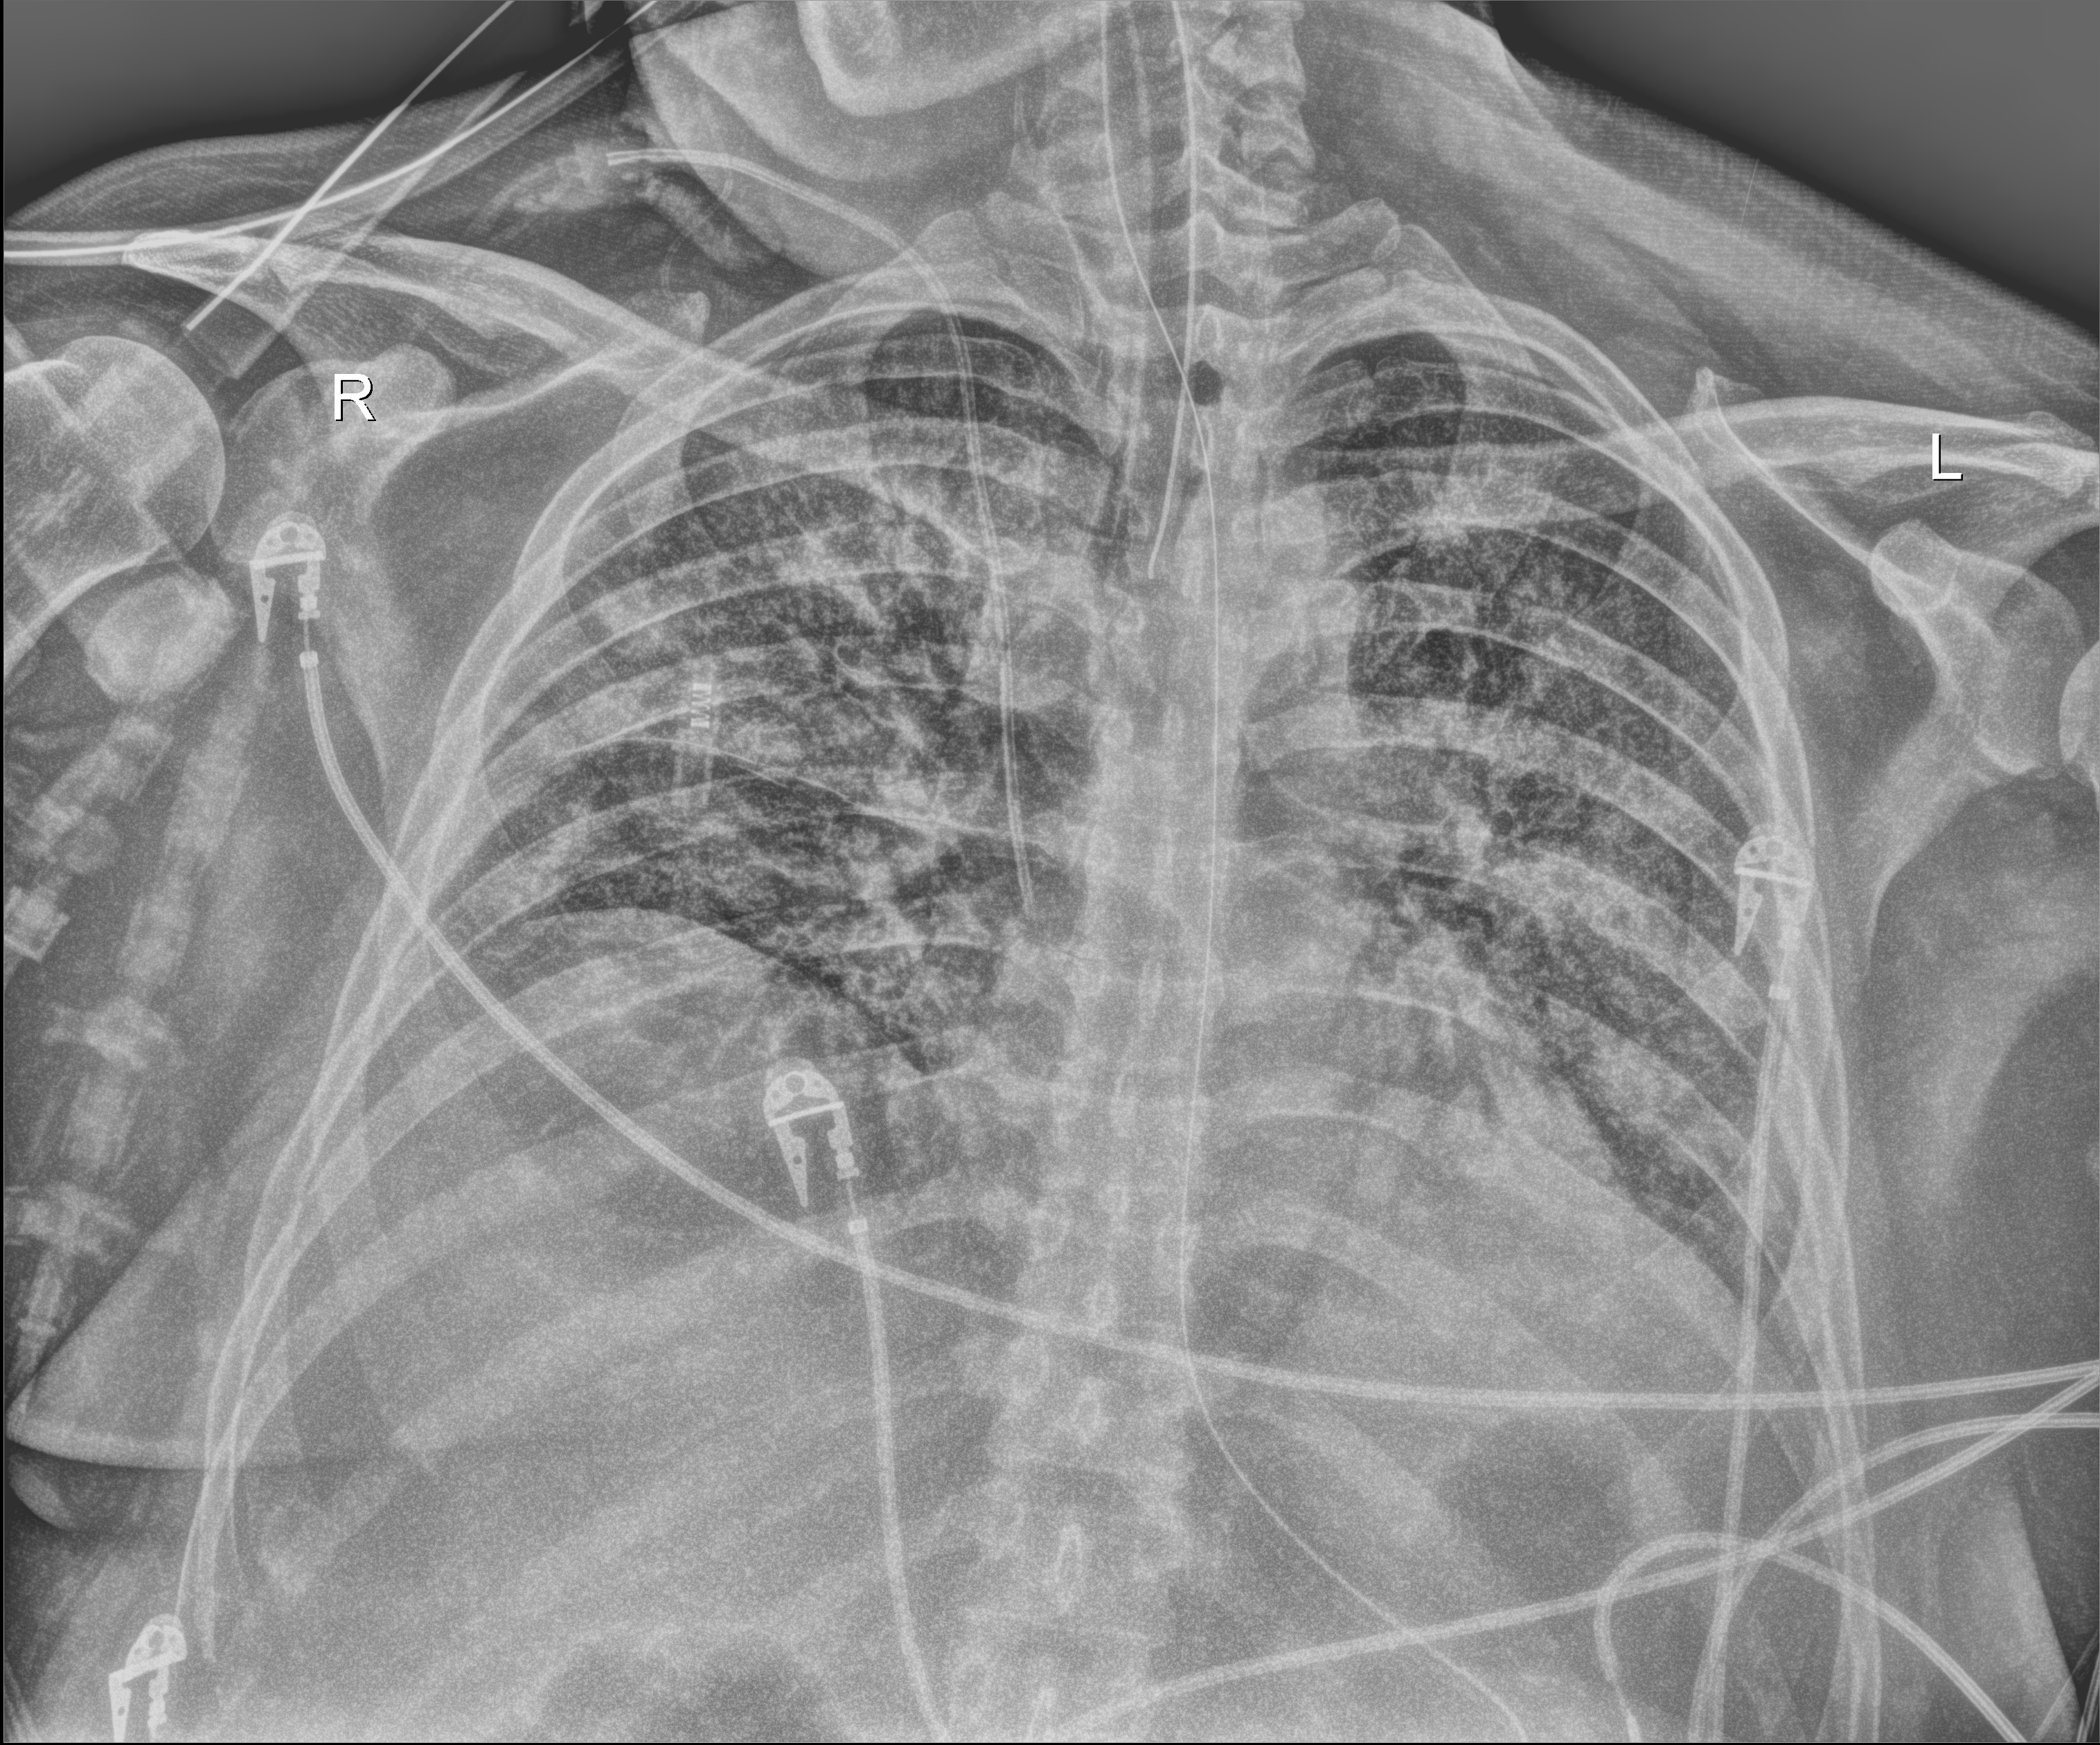
Chest radiograph; anteroposterior (AP) projection. Patient hospitalised with COVID-19; male, aged 18–59 years.
From the hospital-stay record, not from the radiograph (when in the stay this image was taken is not recorded): mechanically ventilated during this hospital stay: yes; admitted to intensive care during this hospital stay: yes.